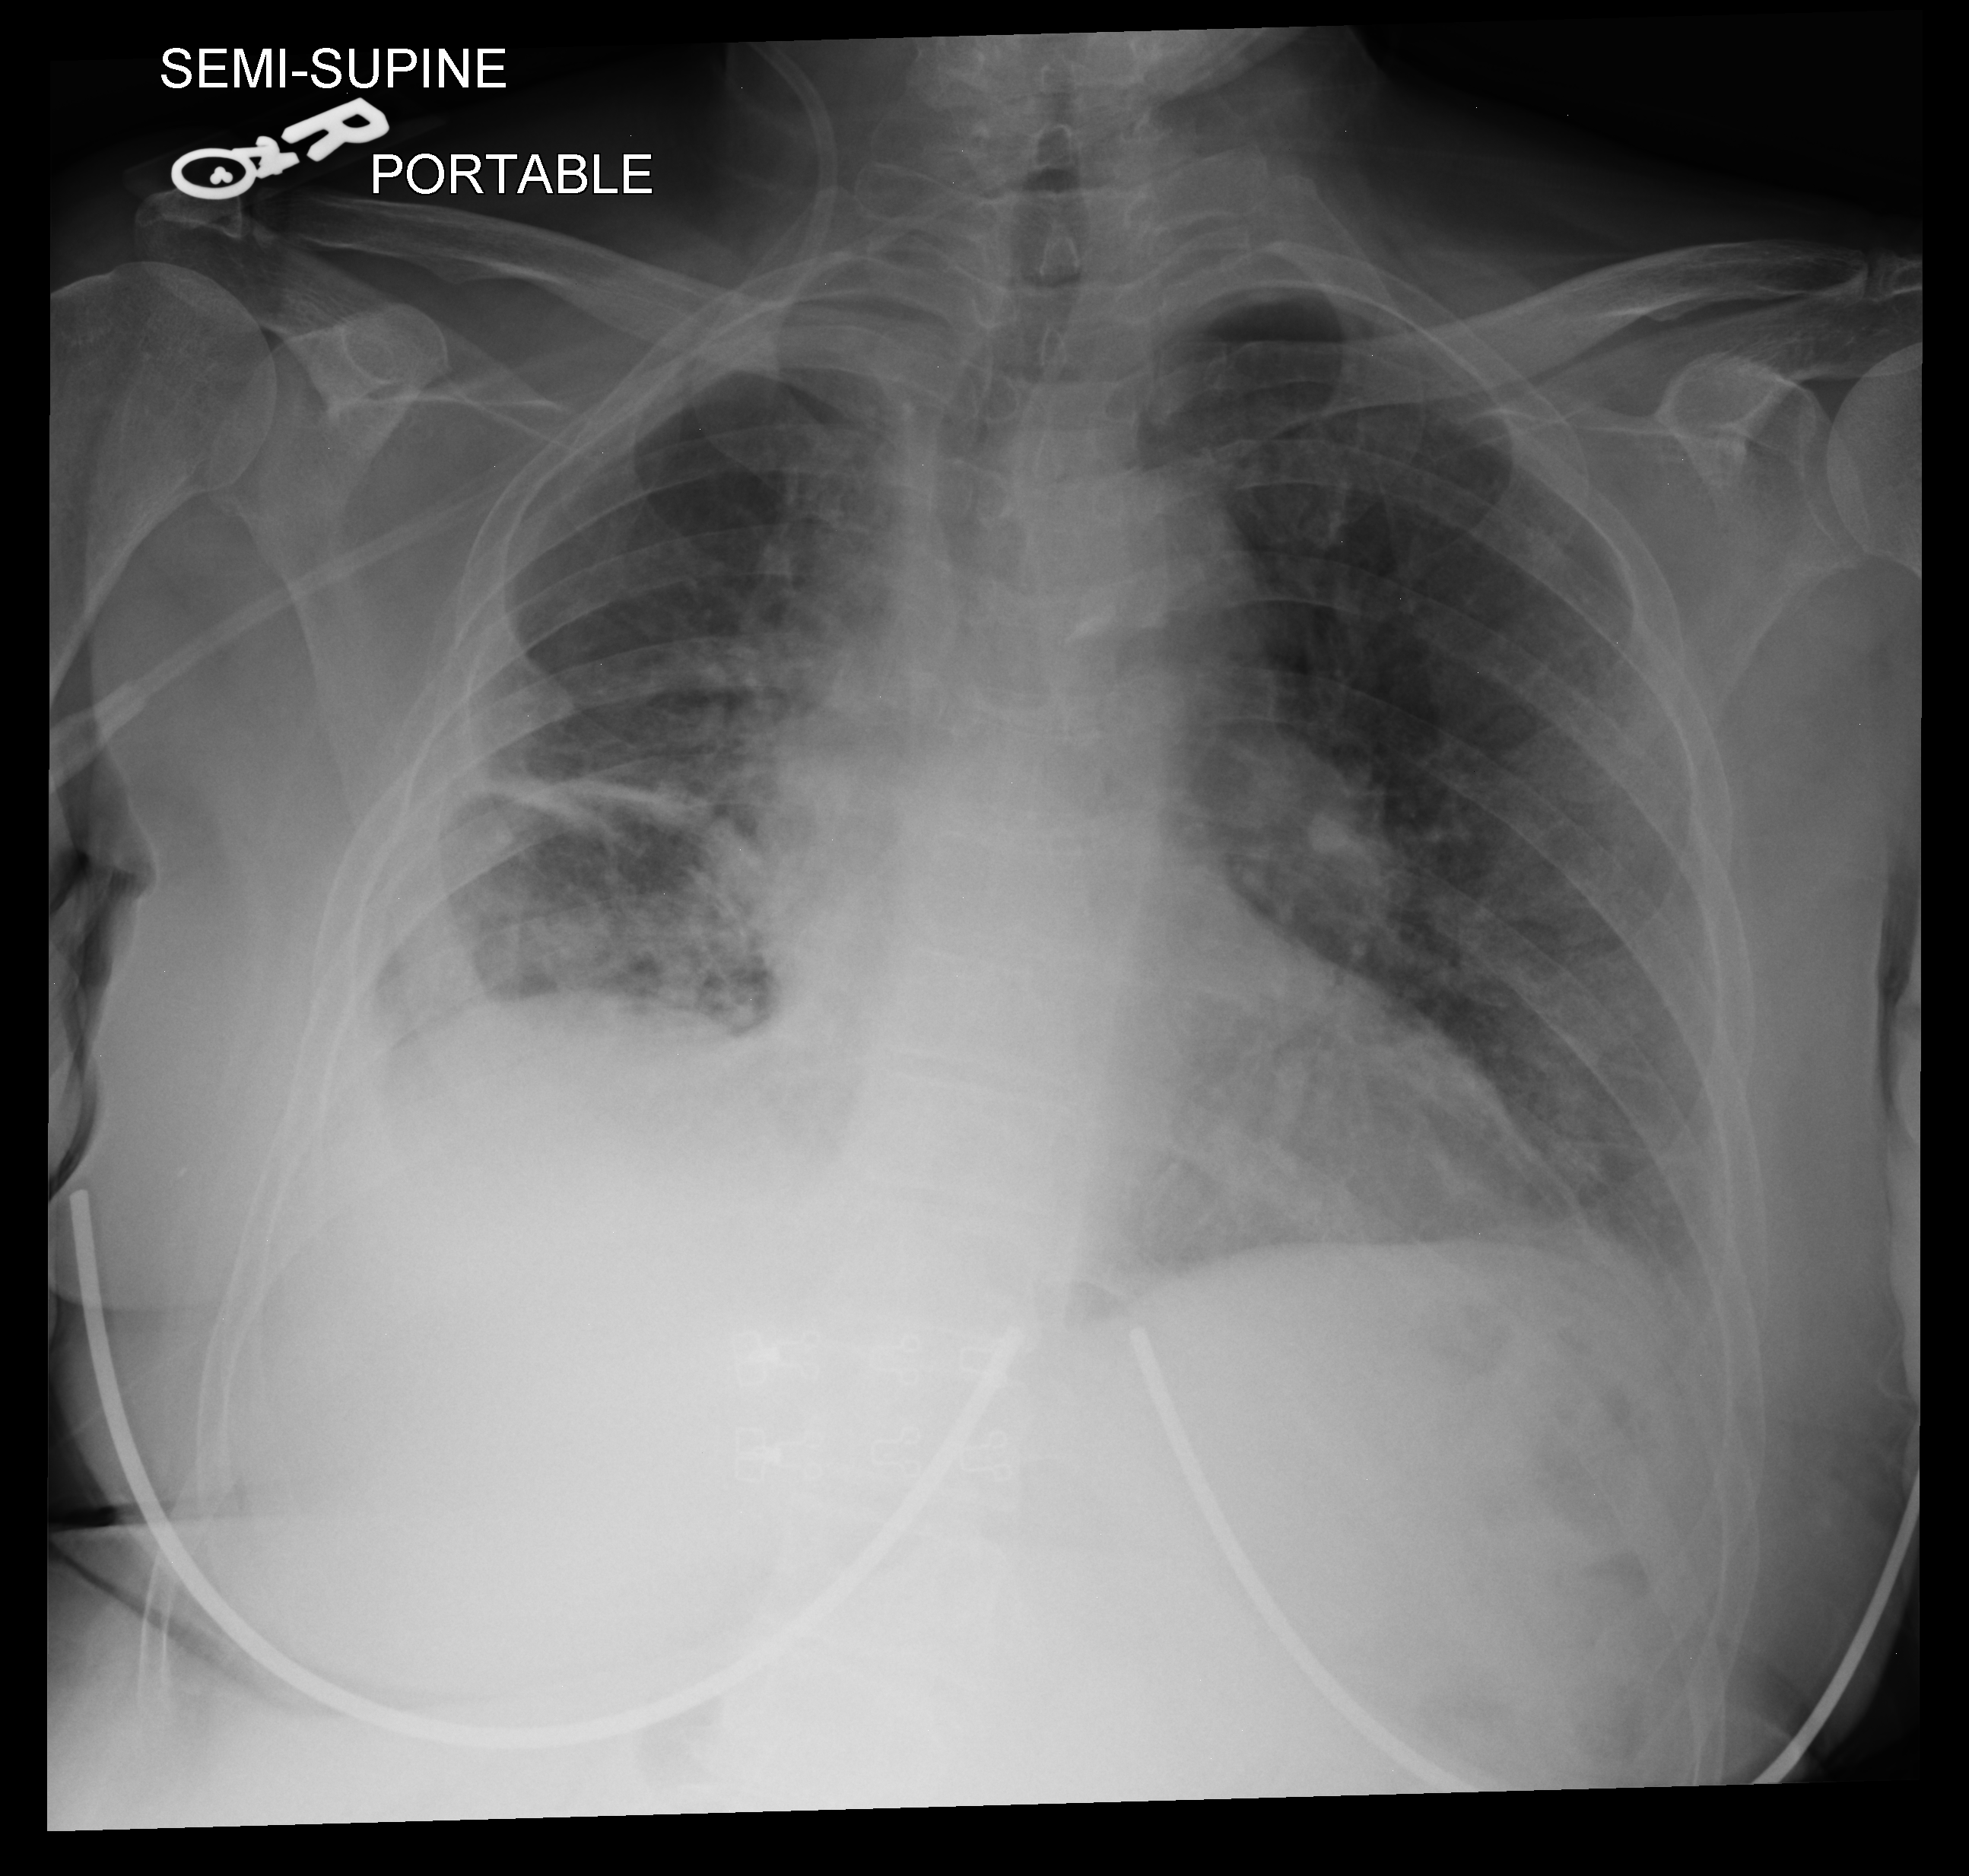
Bedside chest radiograph (computed radiography), anteroposterior (AP) projection. Patient hospitalised with COVID-19; female, aged 60–74 years.
Hospital-stay facts (about this admission, not read from this image; timing relative to this image not recorded):
- admitted to intensive care during this hospital stay: no